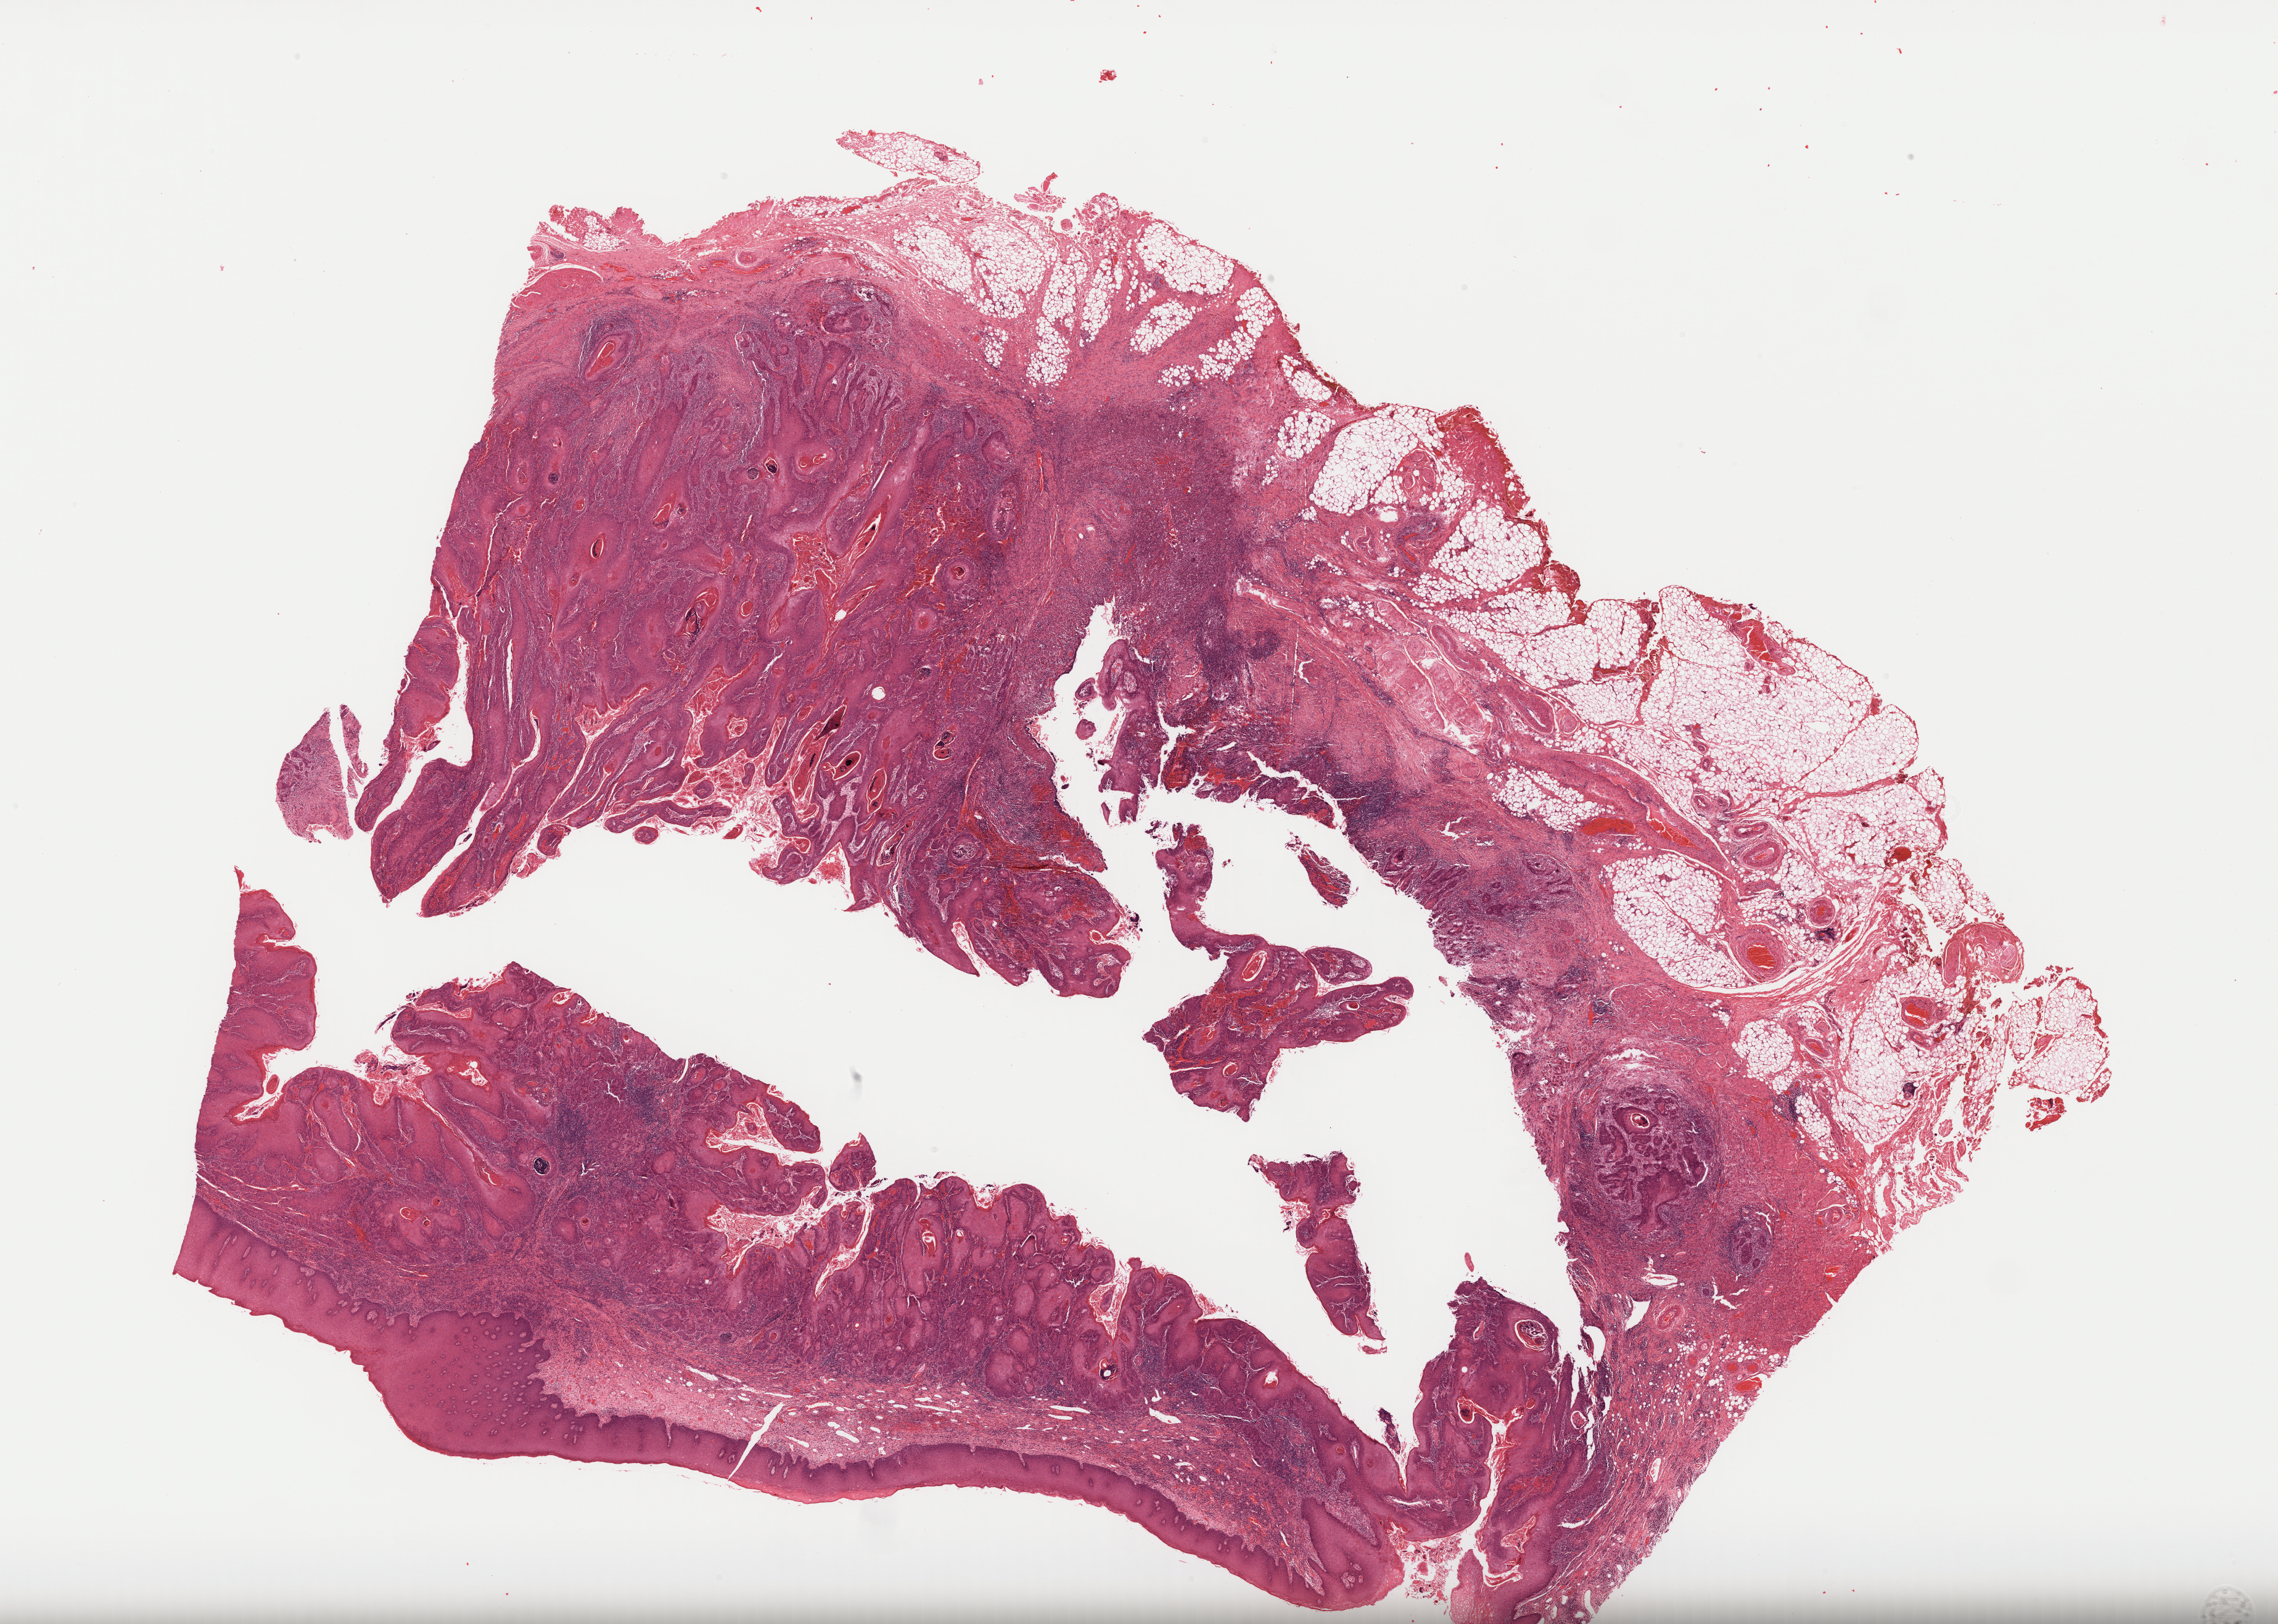
H&E-stained whole-slide image, shown as a low-resolution overview of the whole scanned area (about 29.8 x 21.2 mm, acquisition: 40x scan). FFPE section. Head and neck, primary tumour sample. Patient: male, age at initial diagnosis 69 years.
Histologic diagnosis: Squamous cell carcinoma, NOS (overlapping lesion of lip, oral cavity and pharynx).